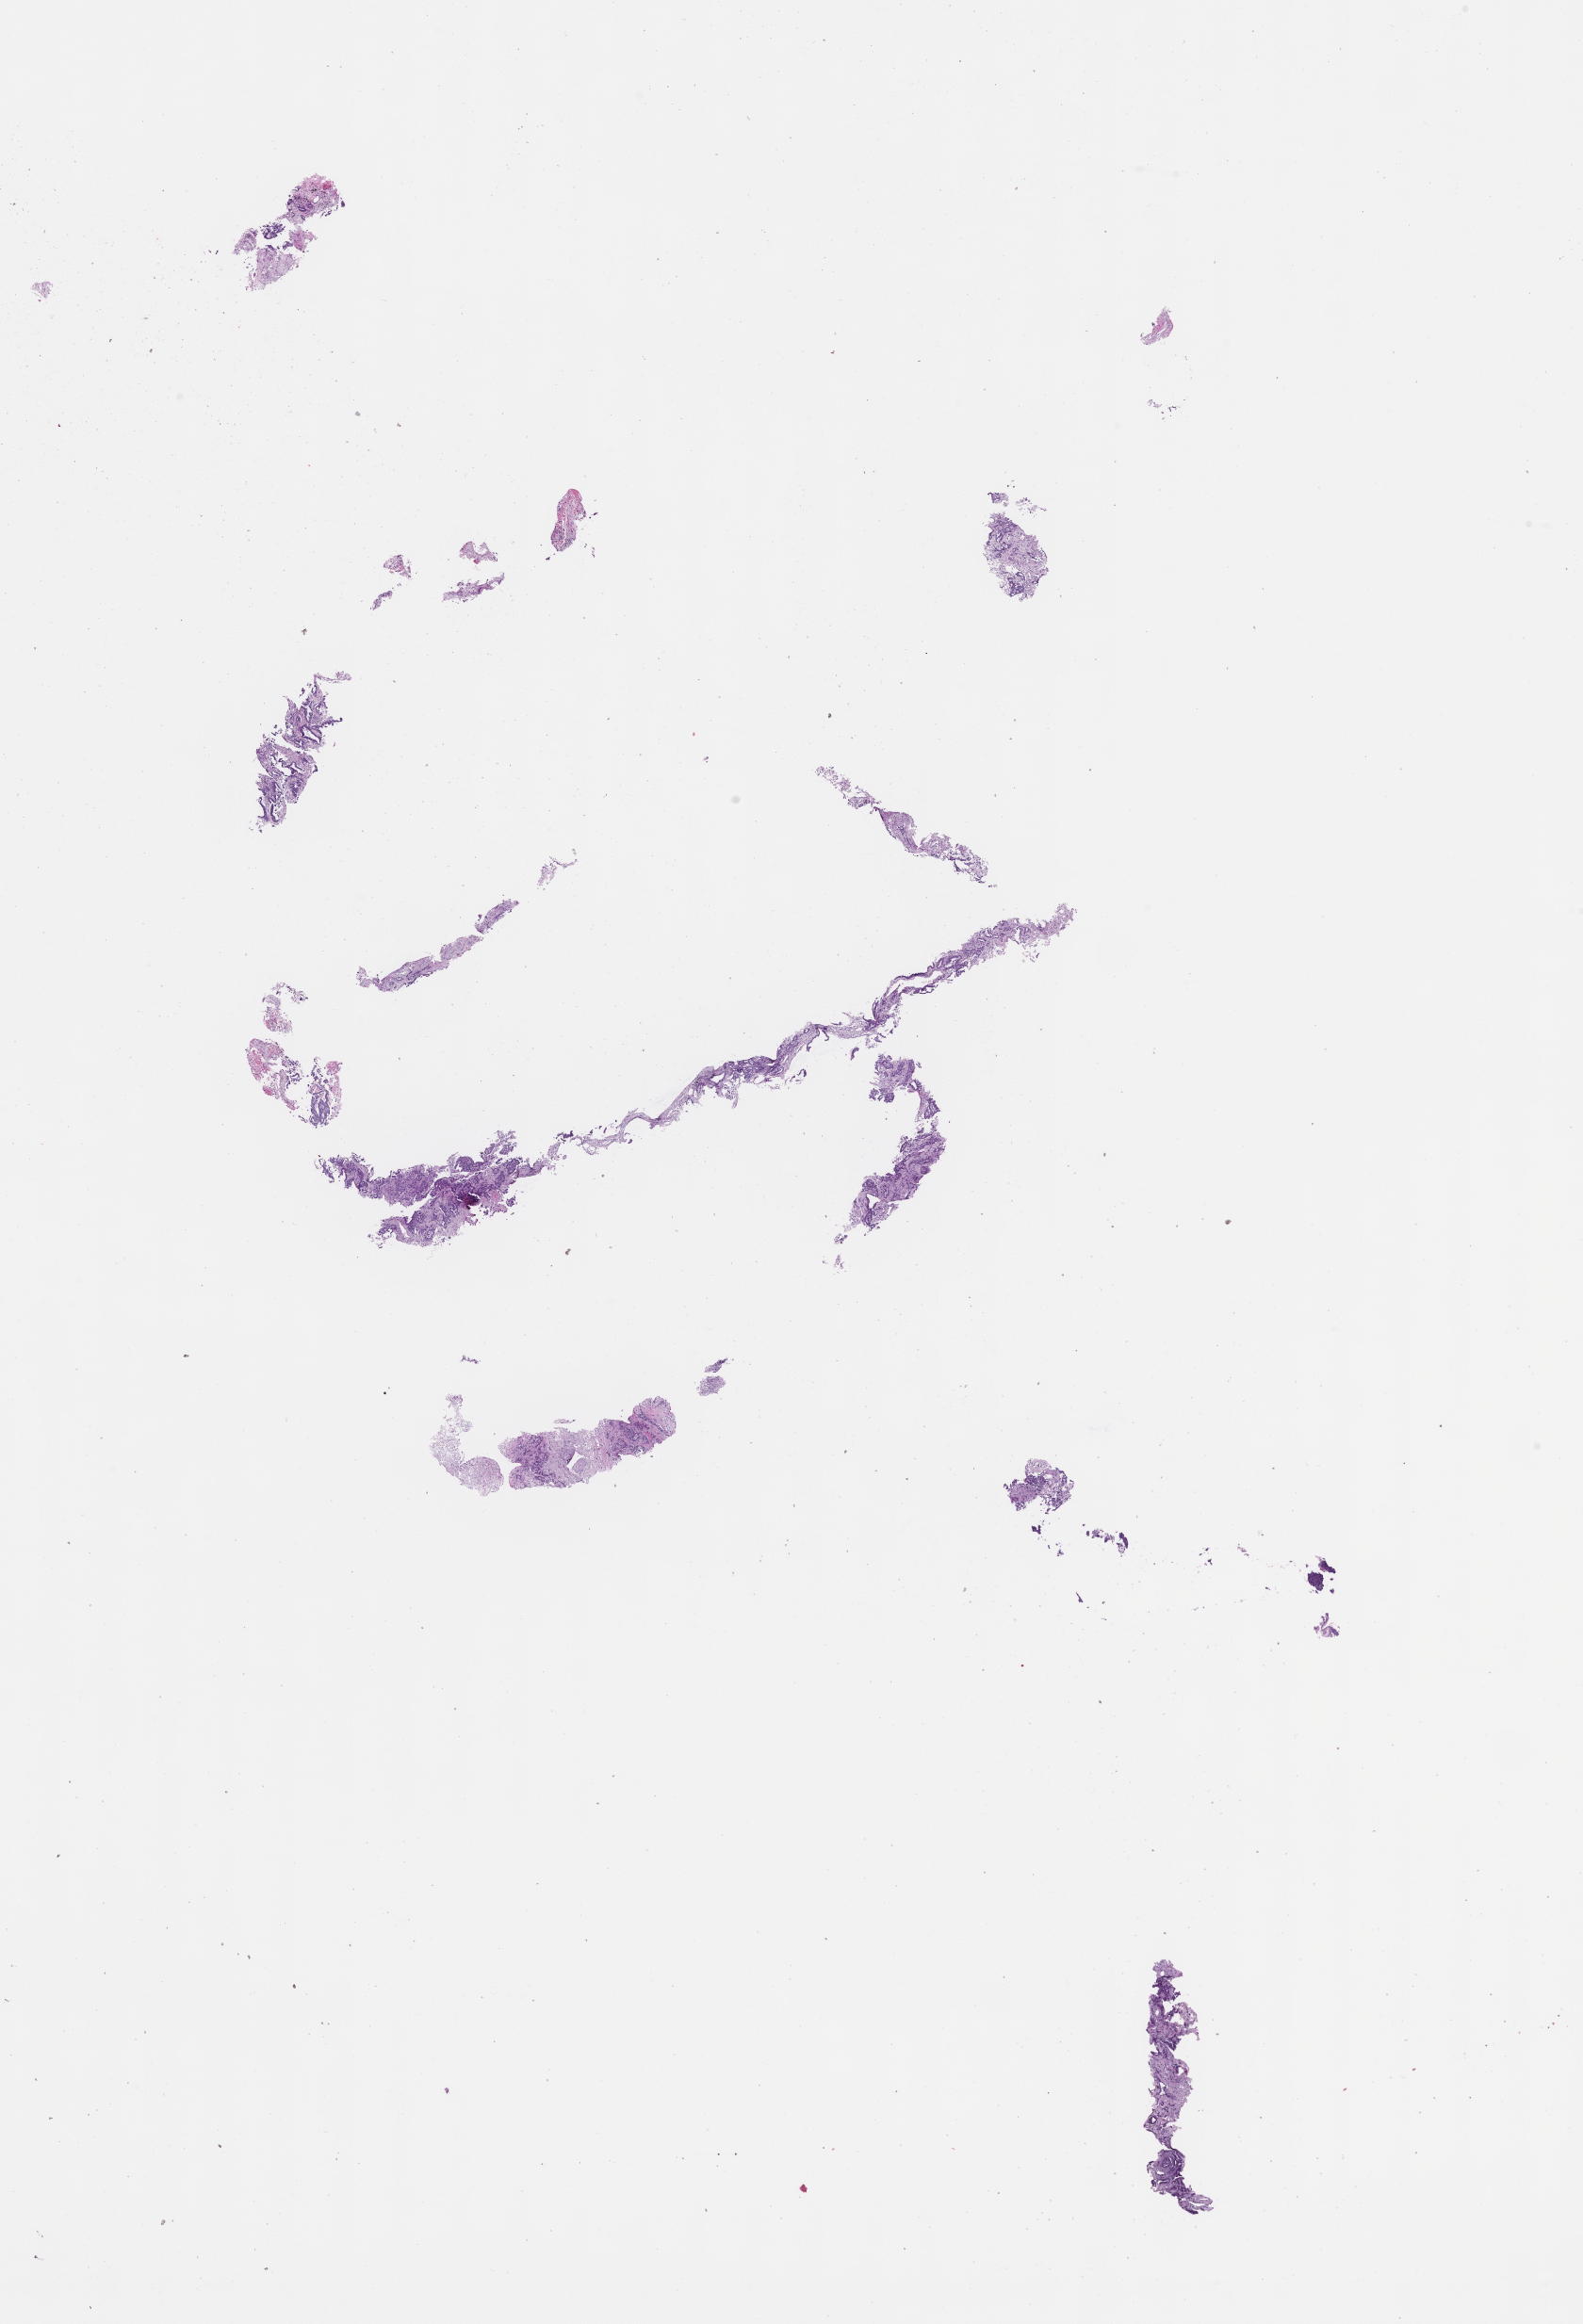
H&E whole-slide image — shown as a low-resolution overview of the whole scanned area (about 13.6 x 19.9 mm), formalin-fixed, paraffin-embedded (FFPE) tissue, tissue site: lung. Female patient.
This section: primary tumour tissue. Diagnosis: Non-Small Cell Lung Carcinoma.